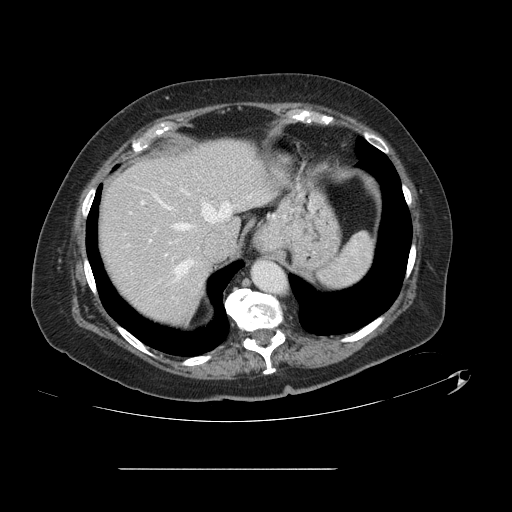
Contrast-enhanced abdominal CT, one axial slice; position 110 of 148 along the scan axis; soft-tissue window (W 400 / L 40 HU); 2.5 mm slice thickness; 512 × 512 image matrix, field of view 439 × 439 mm. Female patient, age 75 years. Case-level facts recorded for this patient, not image findings: diagnosis: colorectal cancer liver metastases, imaged before liver resection; multiple liver metastases: no.
Outlined on this slice (expert manual segmentation):
- hepatic veins: bounding box [x1, y1, x2, y2] px = [153, 194, 234, 277]
- liver: [98, 139, 270, 325]
- planned liver remnant (the part of the liver to remain after resection): [98, 139, 269, 325]
- portal vein (with intrahepatic branches): [141, 201, 151, 241]